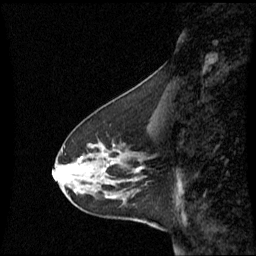
Breast MRI (dynamic contrast-enhanced), one sagittal slice. Slice 25 of 60 in the series (ordered by position). Dynamic contrast-enhanced series, image 2 of 3 at this slice position (ordered by acquisition). 1.5 T. TE 4.2 ms, TR 8.4 ms. 2.2 mm slice thickness. 256 × 256 image matrix, field of view 240 × 240 mm. Female patient, age 45 years. Case-level facts recorded for this patient, not image findings: setting: breast cancer imaged before/during neoadjuvant chemotherapy; receptor status: HR-positive, HER2-negative.
Structures marked on this image (semi-automatically segmented with operator editing):
- analysis volume of interest (the breast-tissue region the enhancement analysis was run in; not a lesion): box from (x=60, y=126) to (x=149, y=215) px
- tumour enhancement mask (voxels above the 70 % enhancement threshold inside the analysis volume of interest): (x=78, y=156)–(x=113, y=199)